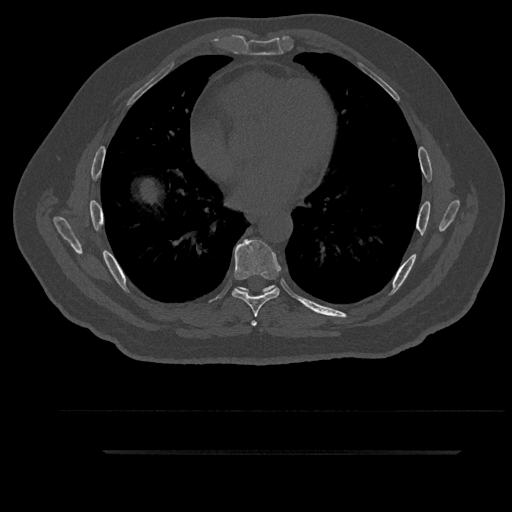
CT including the spine, one axial slice. 120 kVp. Bone window (W 1800 / L 400 HU). 0.5 mm slice thickness. 512 × 512 image matrix, field of view 432 × 432 mm. Patient: male, 63 years. Case-level facts recorded for this patient, not image findings: primary cancer: renal; vertebrae with lytic lesions (as recorded): T8.
Annotated regions visible in this slice (semi-automatic segmentation, software-assisted and operator-edited):
- T6 vertebra: bounding box <235,286,275,326> (left, top, right, bottom; pixels)
- T7 vertebra: <232,239,282,317>
- T8 vertebra: <241,285,275,291>